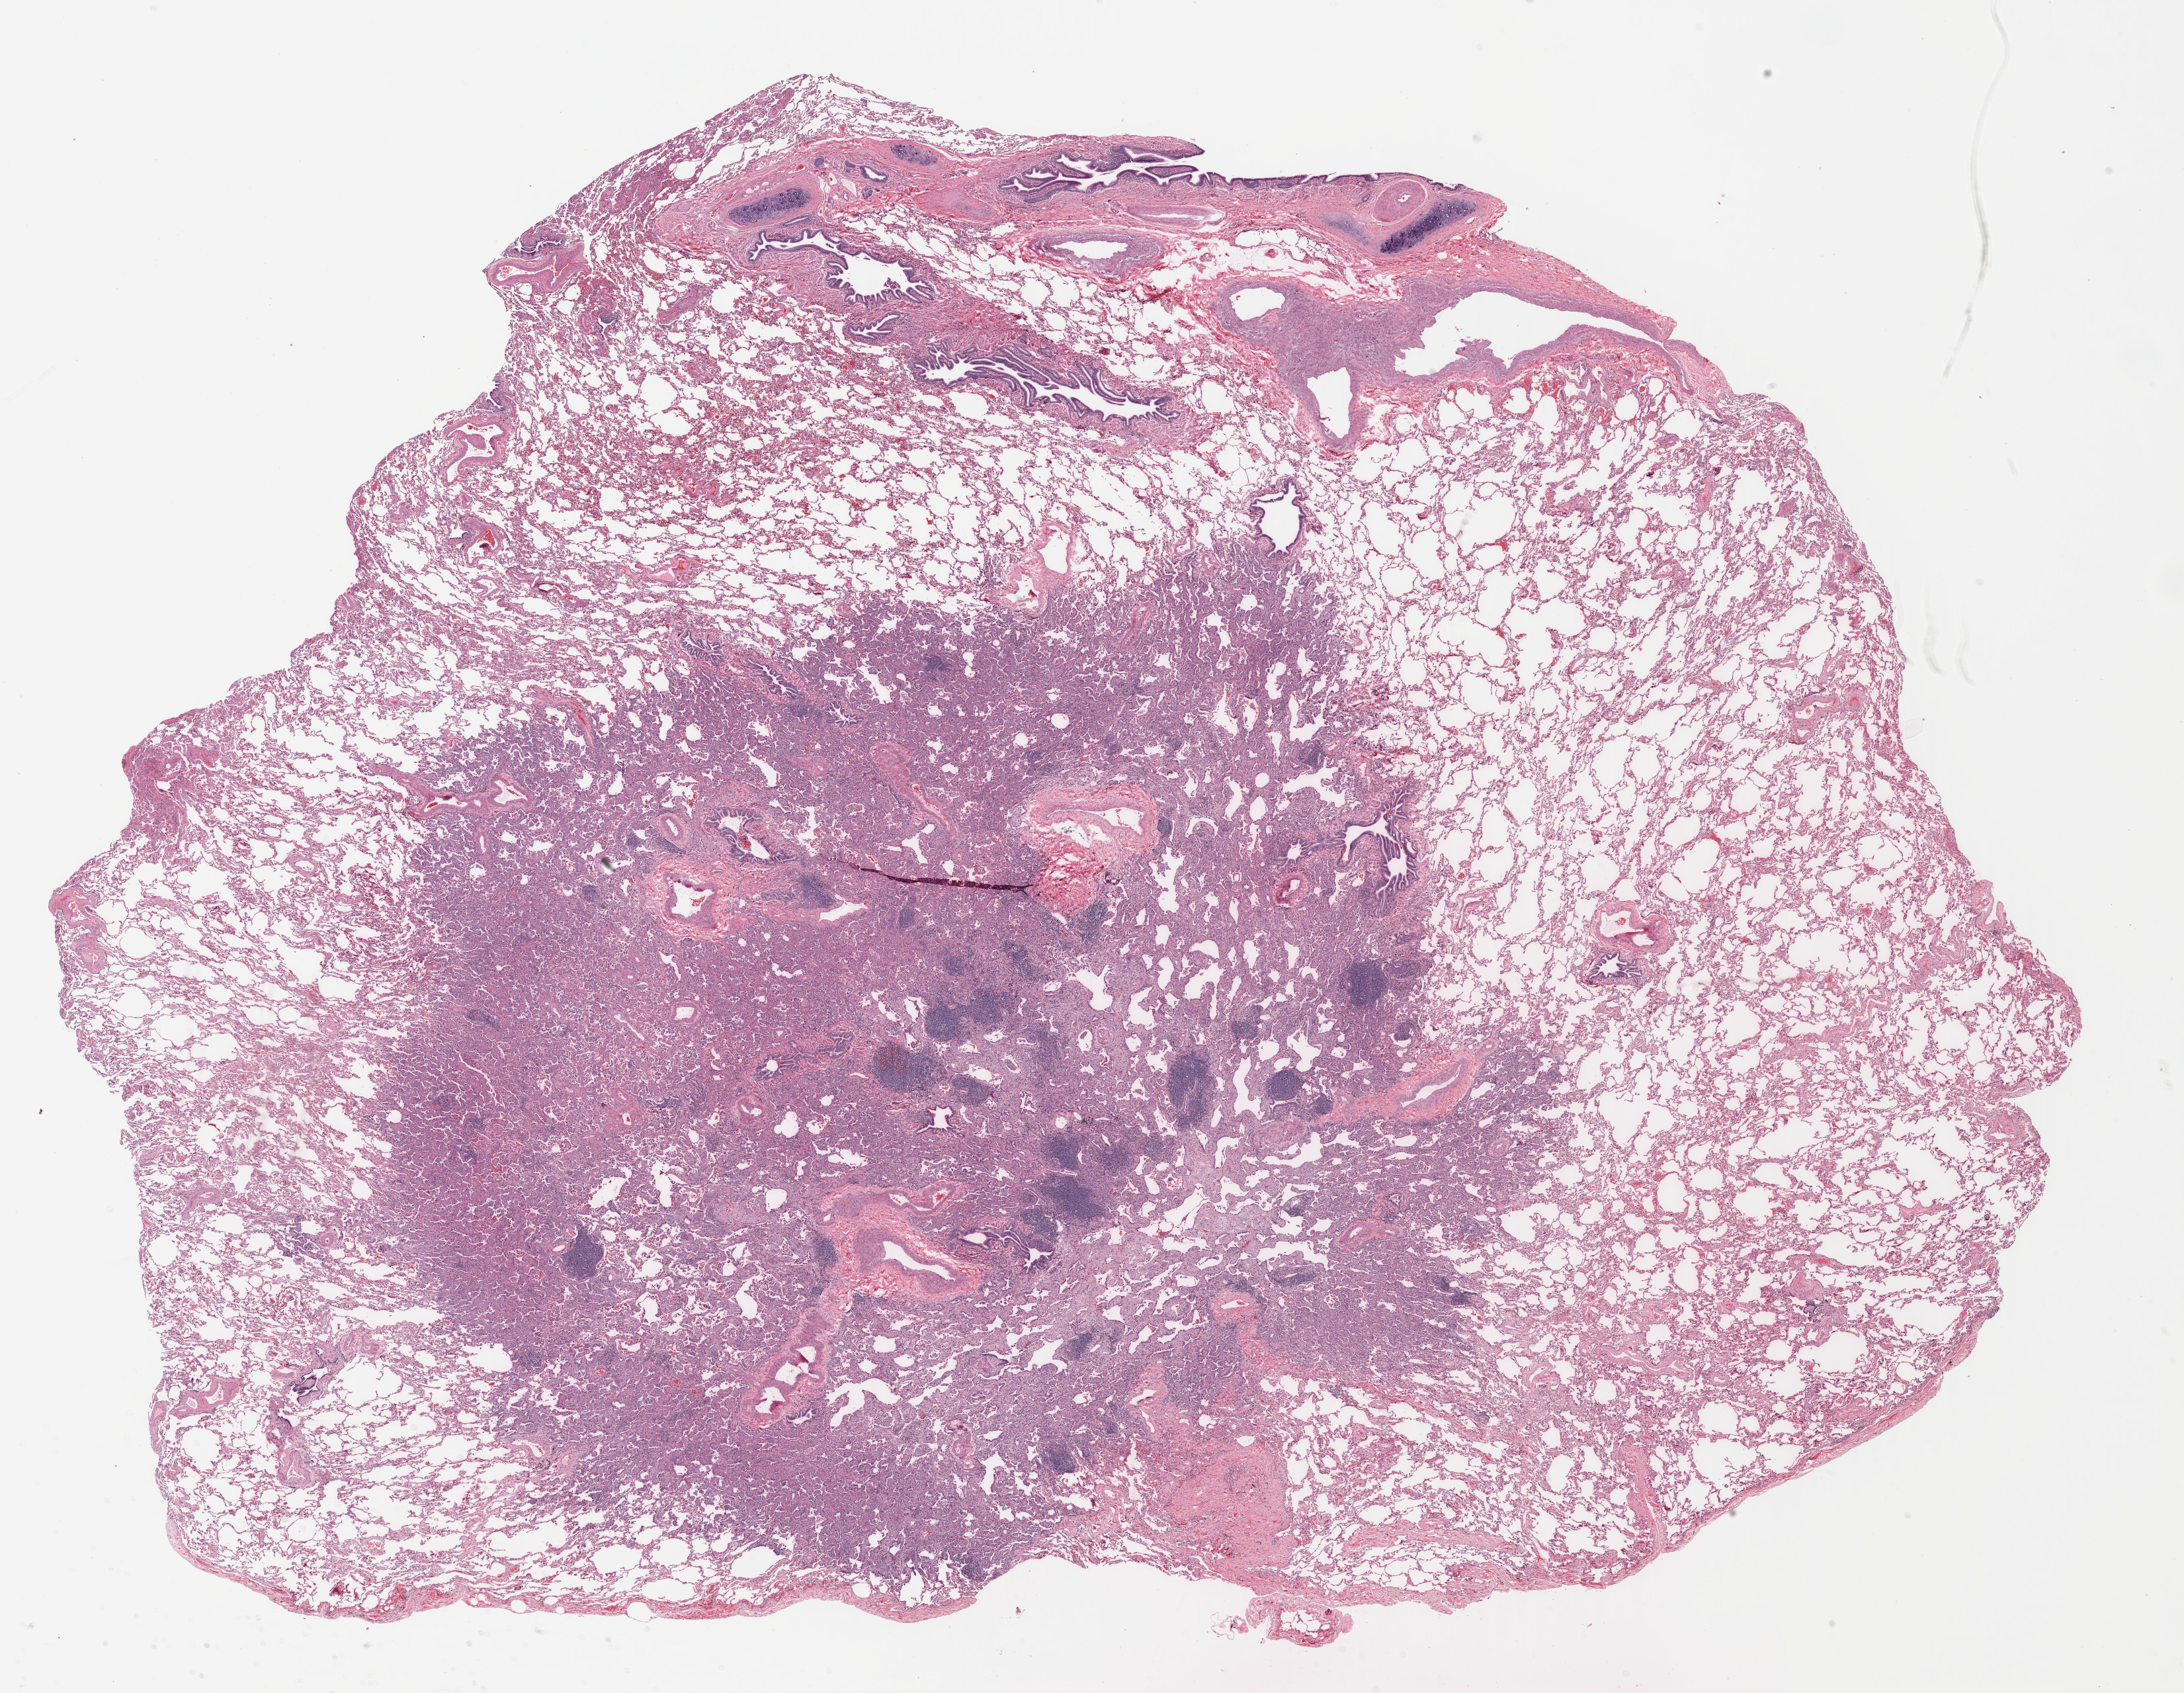
Hematoxylin and eosin (H&E) stained whole-slide image, a low-resolution overview of the entire scanned area, about 26.0 x 20.1 mm, formalin-fixed paraffin-embedded (FFPE) diagnostic section, sample: primary tumour, lung. Female patient; age at initial diagnosis 55 years.
Diagnosis: Bronchiolo-alveolar carcinoma, non-mucinous (lower lobe, lung).